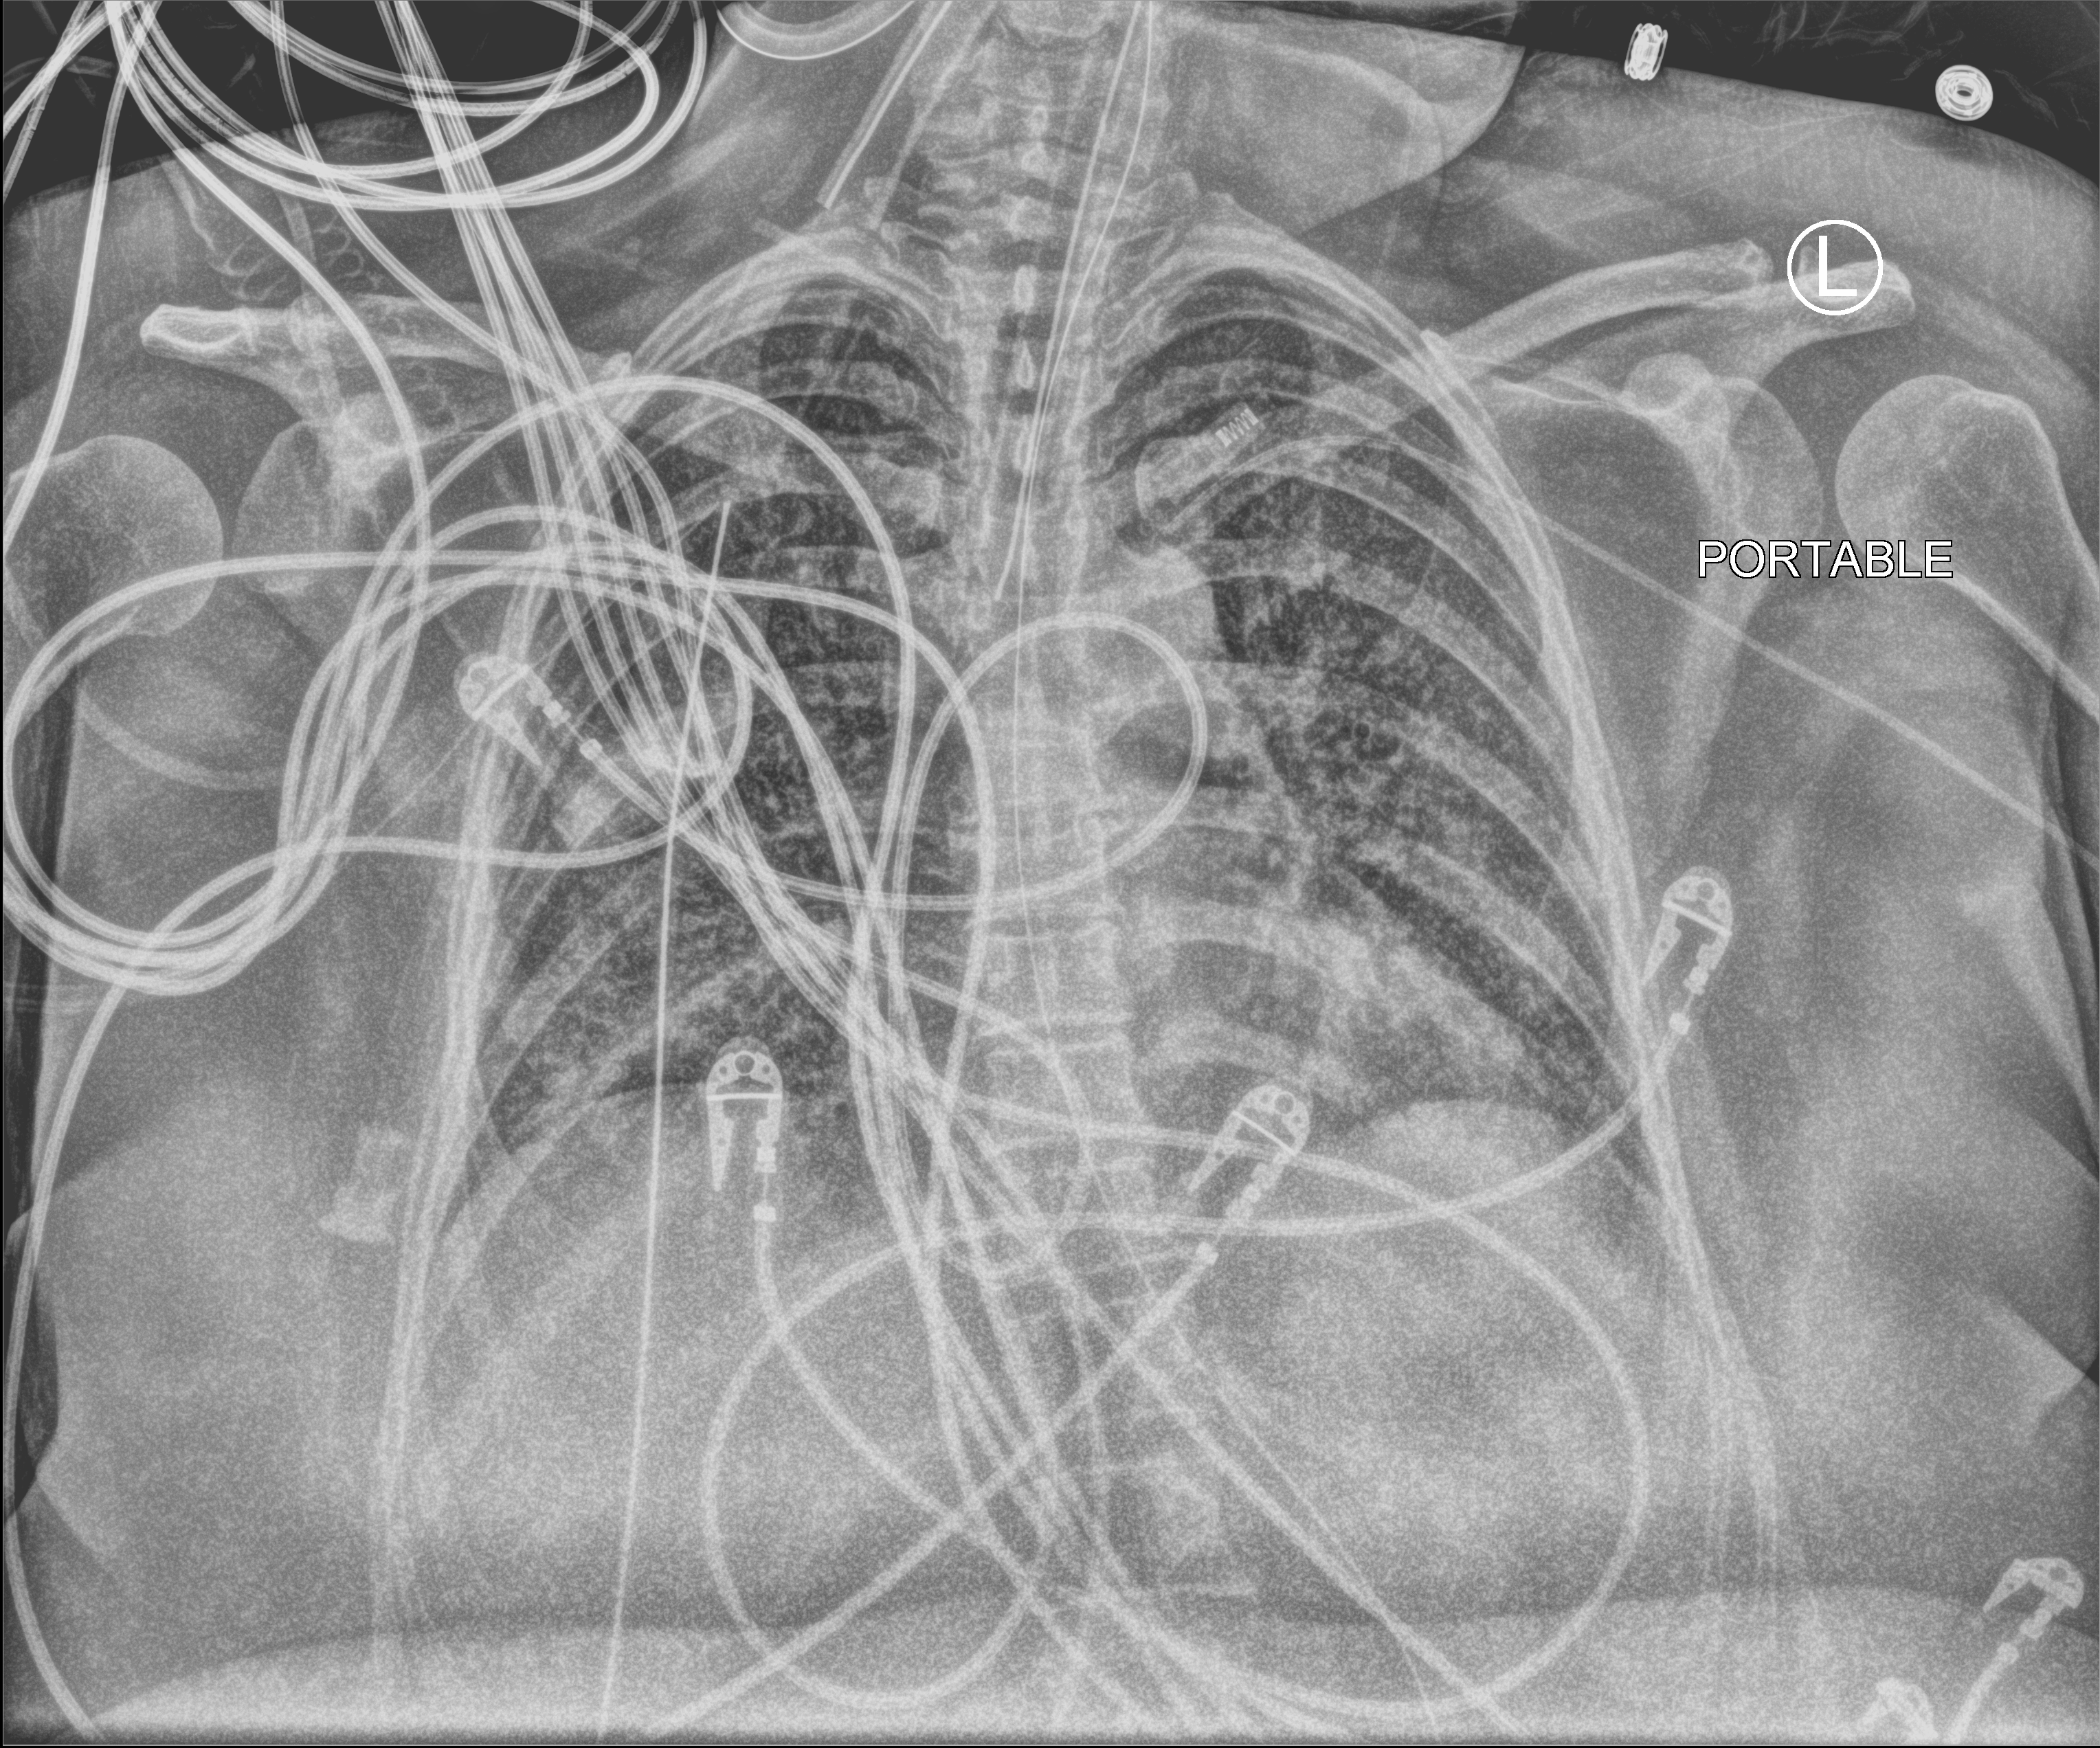
Portable chest radiograph. Female patient hospitalised with COVID-19, age 18–59 years.
Hospital-stay facts (about this admission, not read from this image; timing relative to this image not recorded):
- COPD (admission record): no